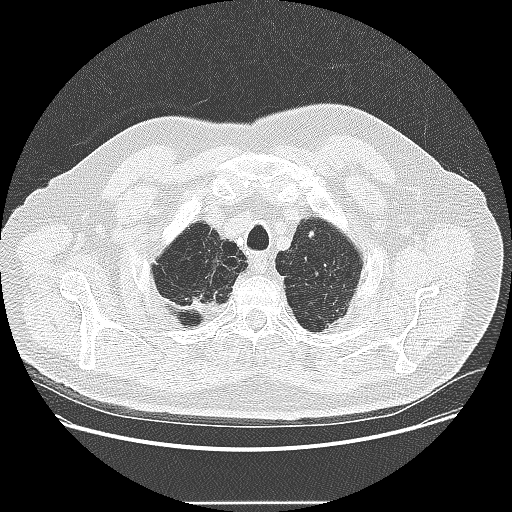
Low-dose screening chest CT, one axial slice; position 221 of 265 along the scan axis; reconstruction kernel LUNG; 120 kVp; lung window (W 1500 / L -600 HU); 512 × 512 image matrix.
Structures marked on this image (expert manual segmentation):
- lesion 1 (tumor, upper lobe of left lung): bounding box <307,230,315,238> (left, top, right, bottom; pixels)